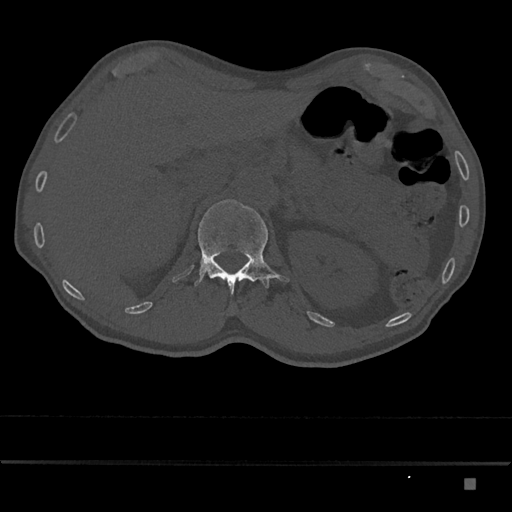
CT including the spine, one axial slice; slice 548 of 797 in the series (ordered by position); 120 kVp; bone window (W 1800 / L 400 HU); 0.5 mm slice thickness; 512 × 512 image matrix. Male patient, age 72 years. Case-level facts recorded for this patient, not image findings: primary cancer: prostate.
Outlined on this slice (semi-automatic segmentation, software-assisted and operator-edited):
- L1 vertebra: bounding box <194,199,289,295> (left, top, right, bottom; pixels)